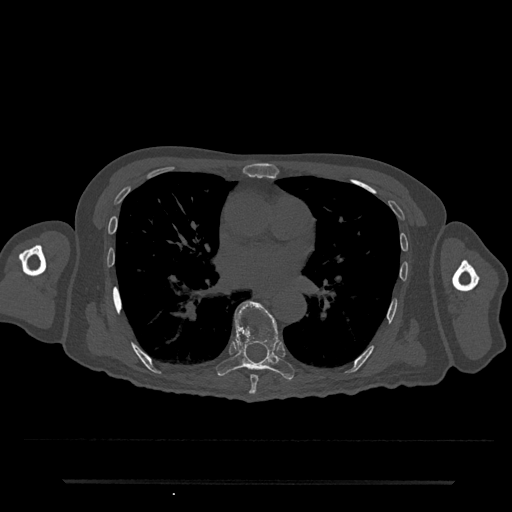
CT including the spine, one axial slice; position 438 of 797 along the scan axis; 120 kVp; bone window (W 1800 / L 400 HU); 0.5 mm slice thickness; 512 × 512 image matrix. Male patient, age 74 years. From the clinical record (not read from this slice): primary cancer: prostate.
Outlined on this slice (semi-automatically segmented with operator editing):
- T7 vertebra: bounding box [x1, y1, x2, y2] px = [249, 375, 259, 395]
- T8 vertebra: [216, 301, 295, 381]